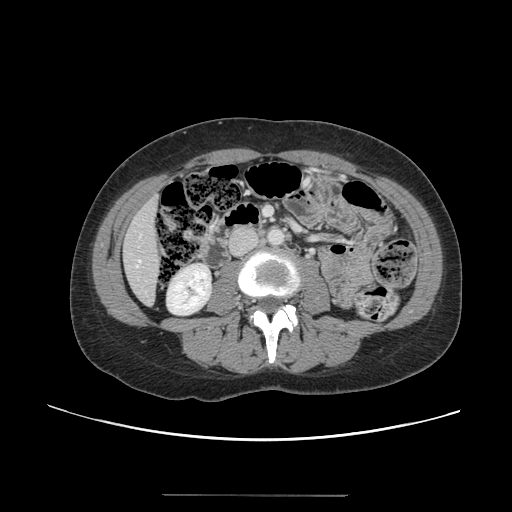
Contrast-enhanced abdominal CT, one axial slice; slice 32 of 144 in the series (ordered by position); 120 kVp; soft-tissue window (W 400 / L 40 HU); 2.5 mm slice thickness; 512 × 512 image matrix, field of view 380 × 380 mm. Female patient, age 53 years. Case-level facts recorded for this patient, not image findings: diagnosis: colorectal cancer liver metastases, imaged before liver resection; multiple liver metastases: yes; largest metastasis: 1.1 cm.
Annotated regions visible in this slice (outlined manually by an expert reader):
- hepatic veins: bounding box [x1, y1, x2, y2] px = [137, 260, 141, 267]
- liver: [124, 201, 162, 303]
- planned liver remnant (the part of the liver to remain after resection): [124, 200, 162, 303]